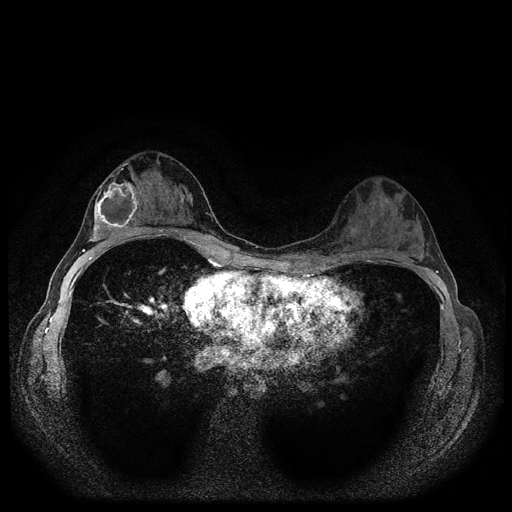
Breast MRI (dynamic contrast-enhanced, multi-phase), one axial slice; position 60 of 116 along the scan axis; dynamic contrast-enhanced series, time point 2 of 5 at this slice position (early post-contrast); 1.5 T; TE 2.7 ms, TR 5.4 ms; 2 mm slice thickness; 512 × 512 image matrix, field of view 320 × 320 mm. Female patient, age 29 years.
Structures marked on this image (semi-automatically segmented with operator editing):
- breast lesion (labelled 'tumour' in the annotation; benign lesions carry a separate 'benign' label): bounding box [x1, y1, x2, y2] px = [88, 180, 140, 243]